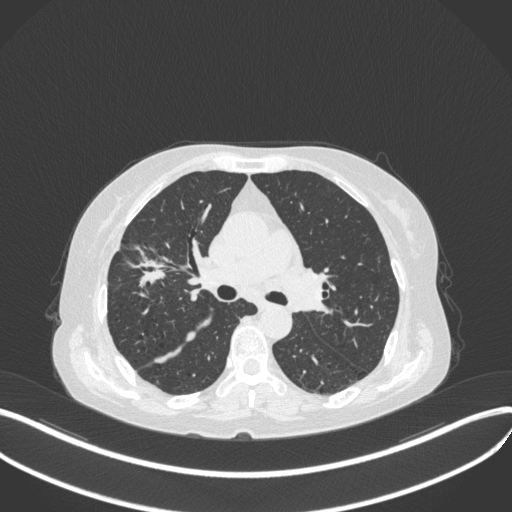
Chest CT, one axial slice. Reconstruction kernel B31f. 120 kVp. Lung window (W 1500 / L -600 HU). 1 mm slice thickness. 512 × 512 image matrix, field of view 400 × 400 mm. Patient: female, 69 years. Case-level facts recorded for this patient, not image findings: clinical TNM (as recorded): T1b N3 M0.
Annotated regions visible in this slice (rectangle marked by the reading radiologist):
- lung tumour (recorded histology: small cell carcinoma): box from (x=121, y=244) to (x=174, y=290) px